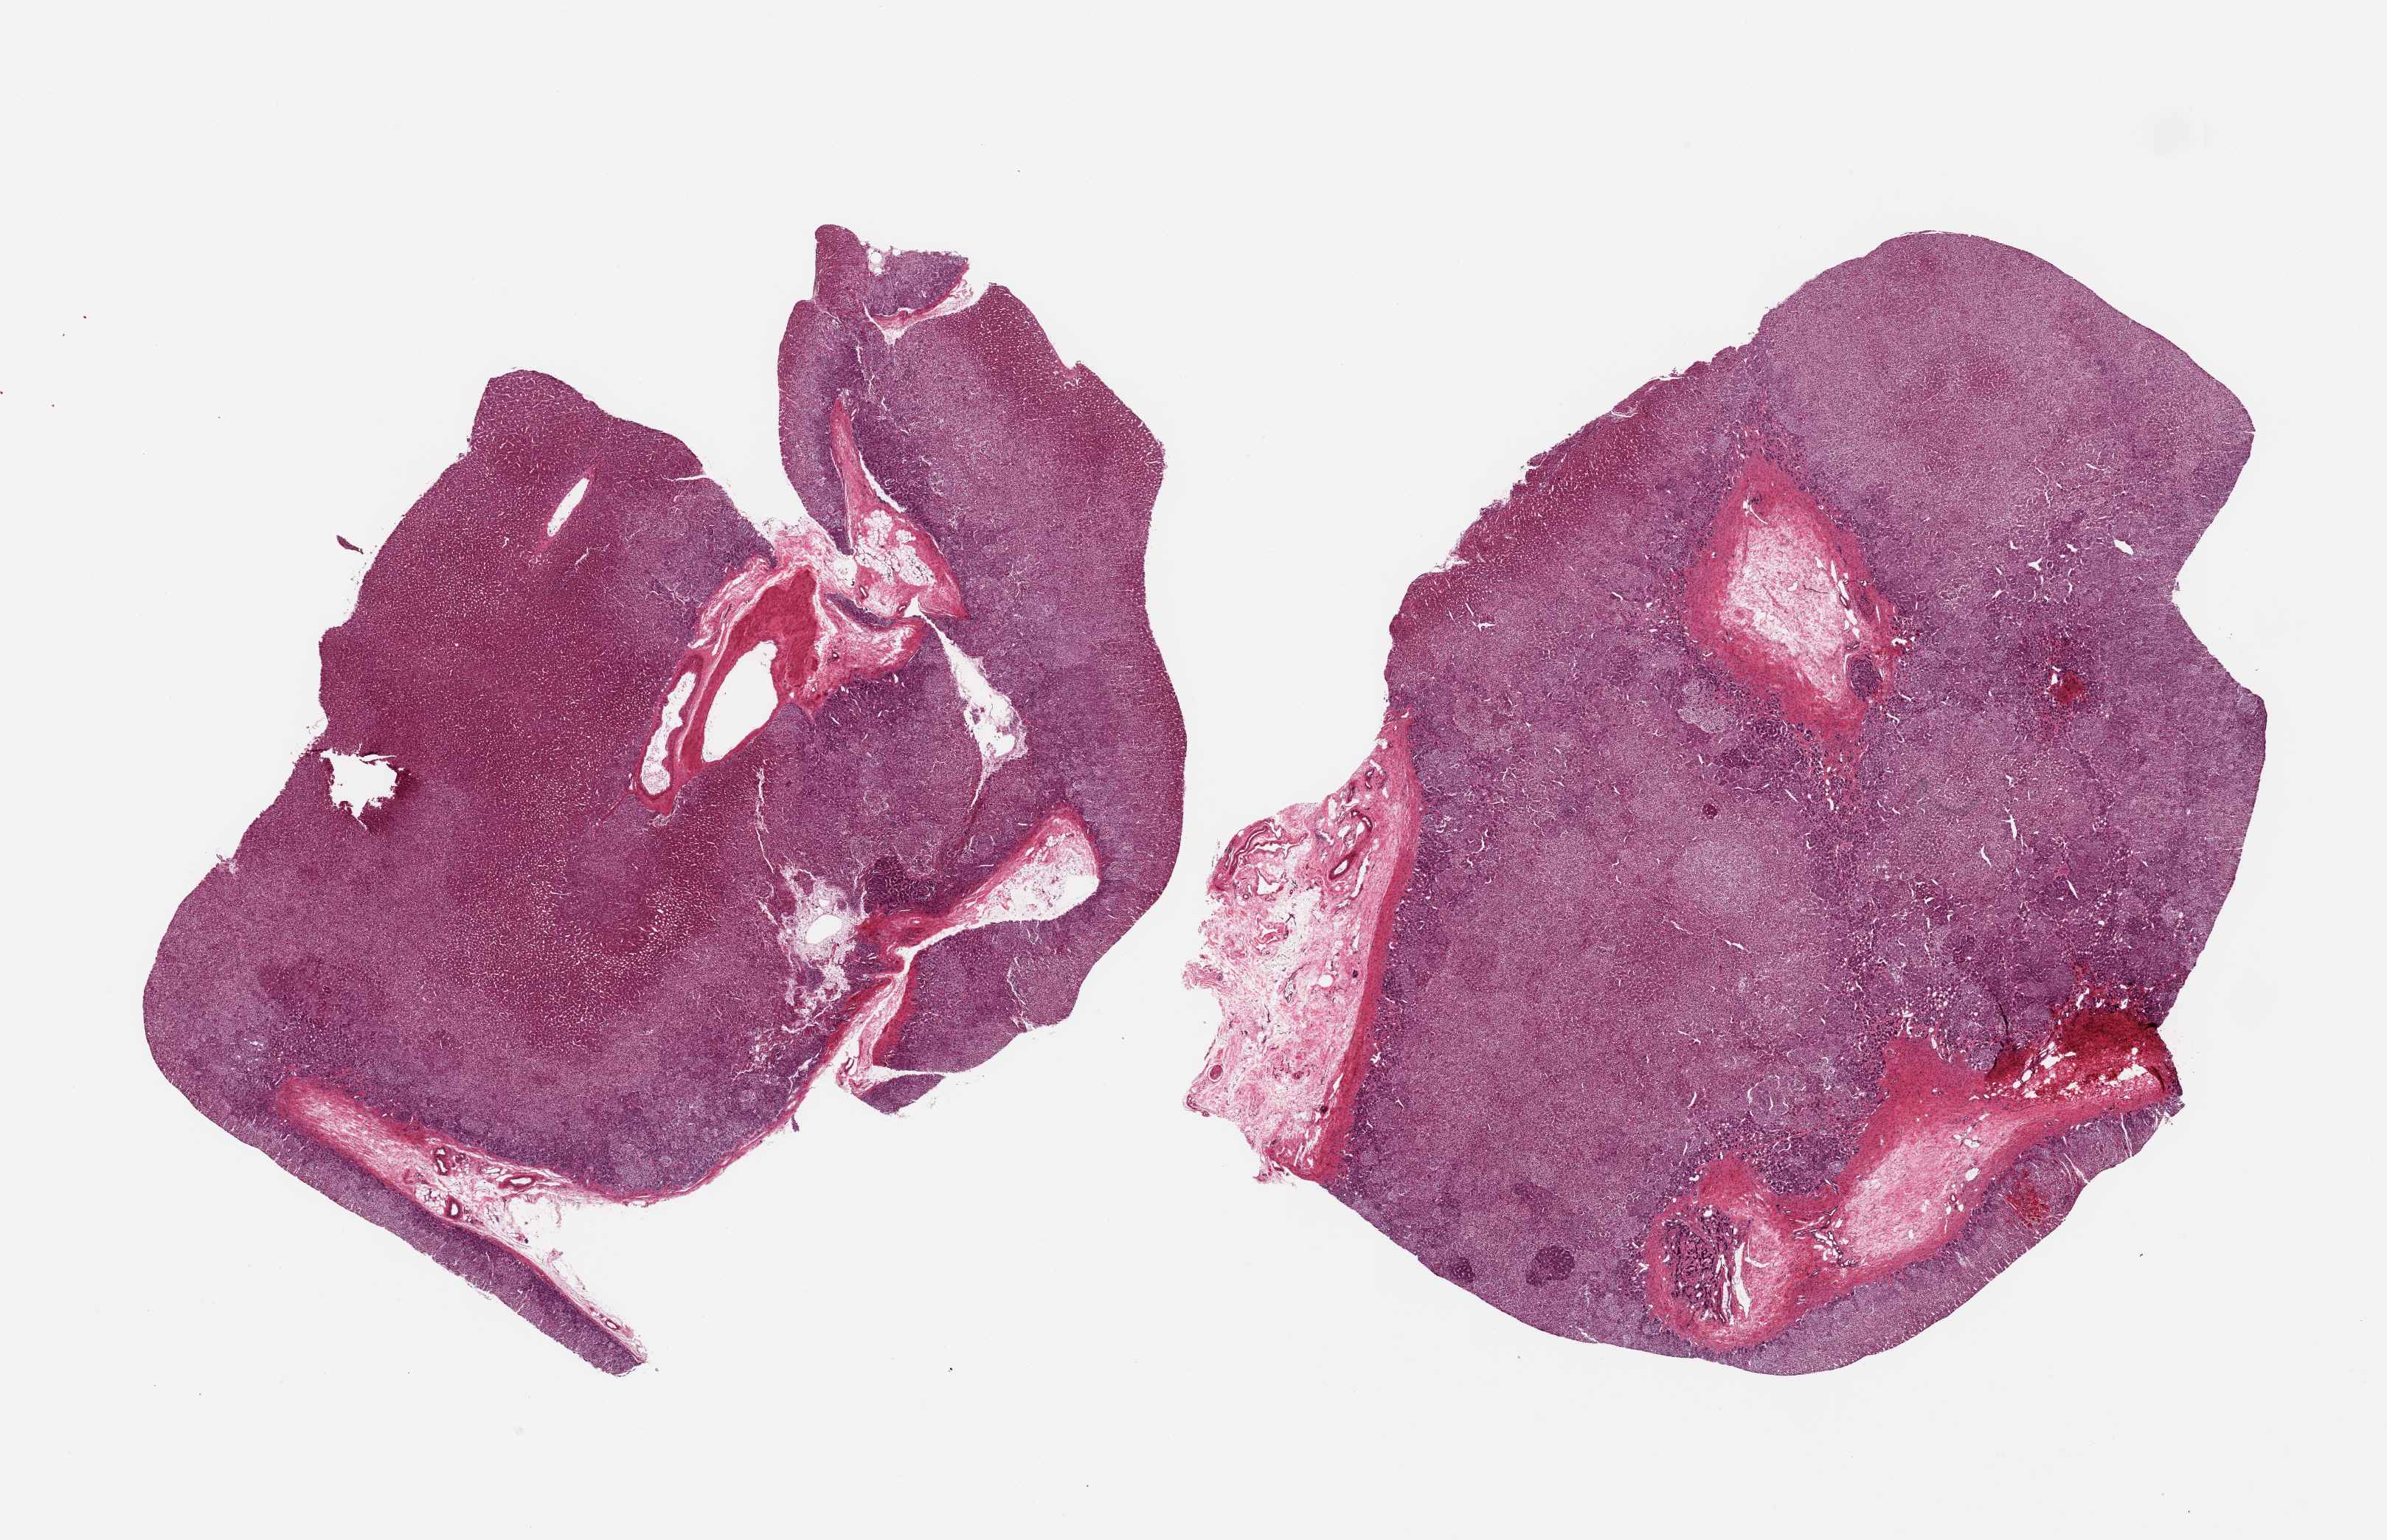
Hematoxylin and eosin (H&E) whole-slide image — low-resolution overview of the scanned area, about 25.6 x 16.5 mm. PAXgene-fixed paraffin-embedded (PFPE) section. Sampled site (target tissue): adrenal gland. Donor tissue sample. Female donor.
Reviewer comment on this tissue sample: 2 pieces, cortex, ~10% interstitial/adherent fat/vascular elements.